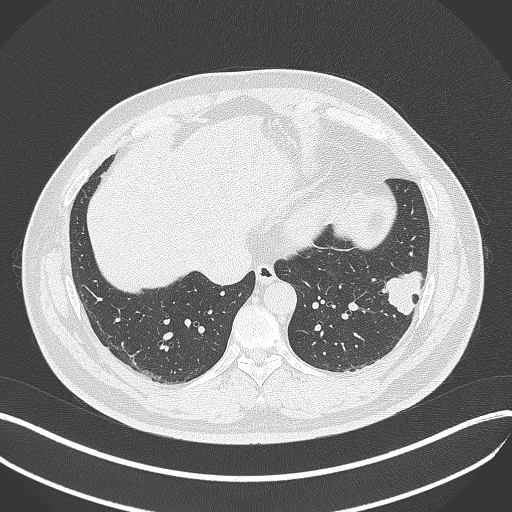
Chest CT, one axial slice; slice 125 of 429 in the series (ordered by position); lung window (W 1500 / L -600 HU); 1 mm slice thickness; 512 × 512 image matrix, field of view 400 × 400 mm. Patient: male, 39 years. From the clinical record (not read from this slice): clinical TNM (as recorded): T2a N0 M0; histopathological grade: G2-3.
Outlined on this slice (bounding box drawn by a radiologist):
- lung tumour (recorded histology: adenocarcinoma): bounding box <378,265,428,322> (left, top, right, bottom; pixels)